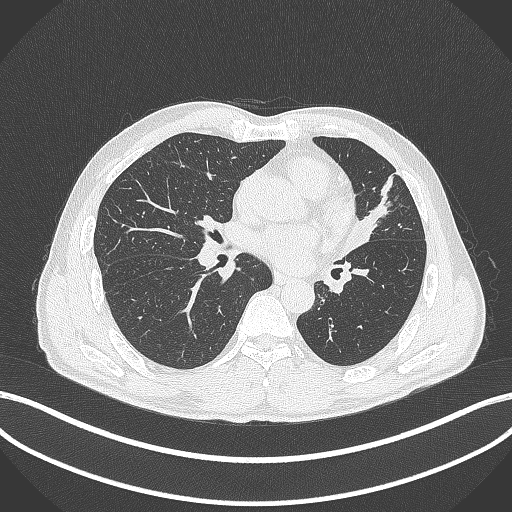
Chest CT, one axial slice. Slice 212 of 429 in the series (ordered by position). 120 kVp. Lung window (W 1500 / L -600 HU). 512 × 512 image matrix, field of view 400 × 400 mm. Patient: male, 57 years. Case-level facts recorded for this patient, not image findings: clinical TNM (as recorded): T2b N0 M0.
Outlined on this slice (rectangle marked by the reading radiologist):
- lung tumour (recorded histology: squamous cell carcinoma): bounding box <343,200,384,255> (left, top, right, bottom; pixels)